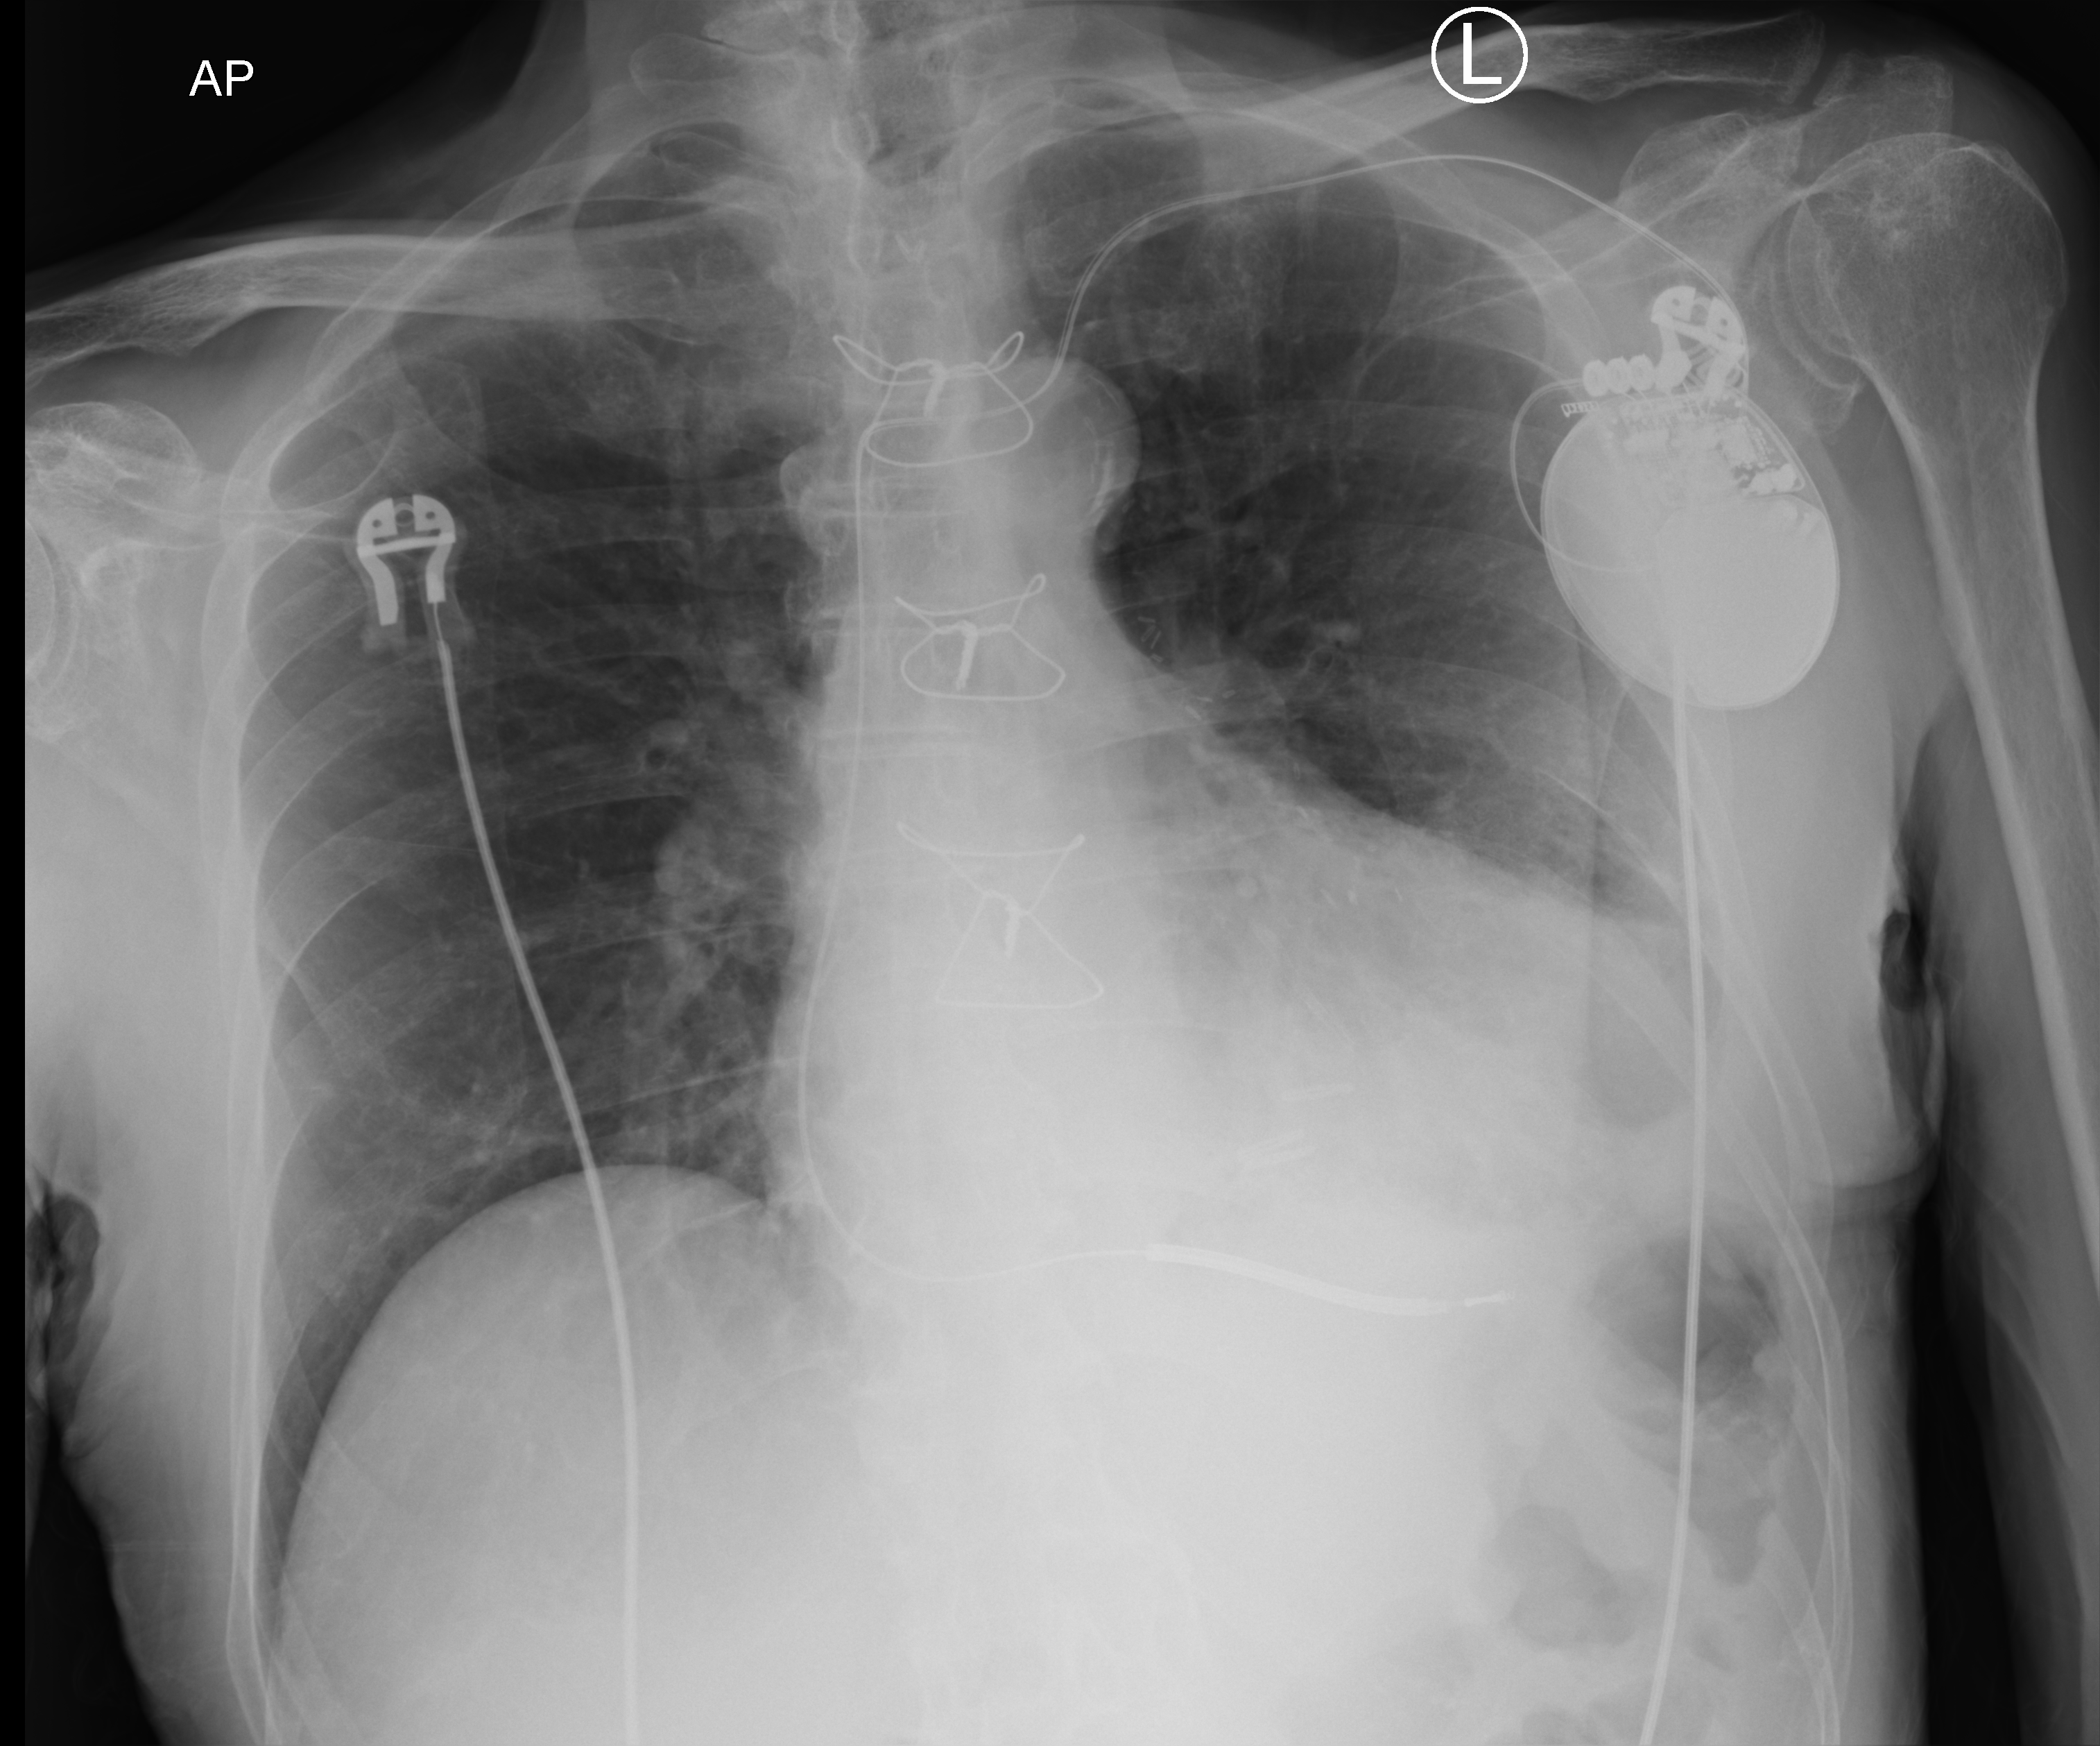
Chest X-ray (portable), anteroposterior (AP) projection. Patient hospitalised with COVID-19; male, aged 75–90 years.
From the hospital-stay record, not from the radiograph (when in the stay this image was taken is not recorded):
- length of hospital stay: 25 days
- admitted to intensive care during this hospital stay: no